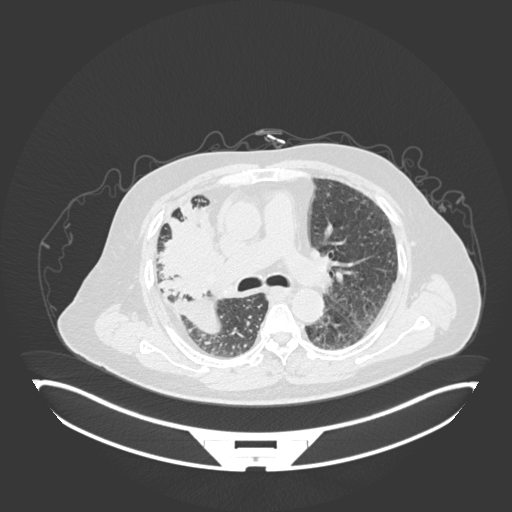
Chest CT, one axial slice. Position 104 of 201 along the scan axis. Reconstruction kernel B30f. Lung window (W 1500 / L -600 HU). 1 mm slice thickness. 512 × 512 image matrix. Patient: male, 69 years. Case-level facts recorded for this patient, not image findings: clinical TNM (as recorded): T4 N3 M1.
Annotated regions visible in this slice (rectangle marked by the reading radiologist):
- lung tumour (recorded histology: adenocarcinoma): bounding box <158,202,215,300> (left, top, right, bottom; pixels)